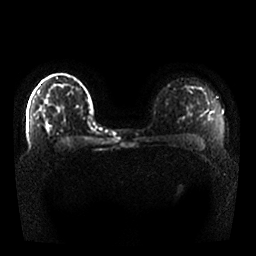
Breast MRI, one axial slice; slice 21 of 25 in the series (ordered by position); diffusion-weighted series; image 2 of 4 stored at this slice position (different b-values; order by instance number); 1.5 T; 4 mm slice thickness; 256 × 256 image matrix, field of view 360 × 360 mm. Female patient.
Structures marked on this image (expert manual segmentation):
- tumour on diffusion-weighted imaging: box from (x=45, y=128) to (x=48, y=131) px